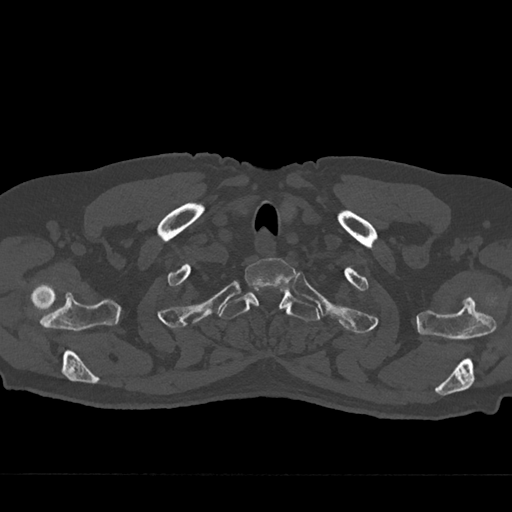
CT including the spine, one axial slice; position 631 of 797 along the scan axis; 120 kVp; bone window (W 1800 / L 400 HU); 0.5 mm slice thickness; 512 × 512 image matrix, field of view 377 × 377 mm. Patient: male, 75 years. Case-level facts recorded for this patient, not image findings: primary cancer: renal; vertebrae with lytic lesions (as recorded): T4.
Outlined on this slice (semi-automatic segmentation, software-assisted and operator-edited):
- T1 vertebra: bounding box [x1, y1, x2, y2] px = [245, 258, 294, 289]
- T2 vertebra: [220, 289, 319, 322]